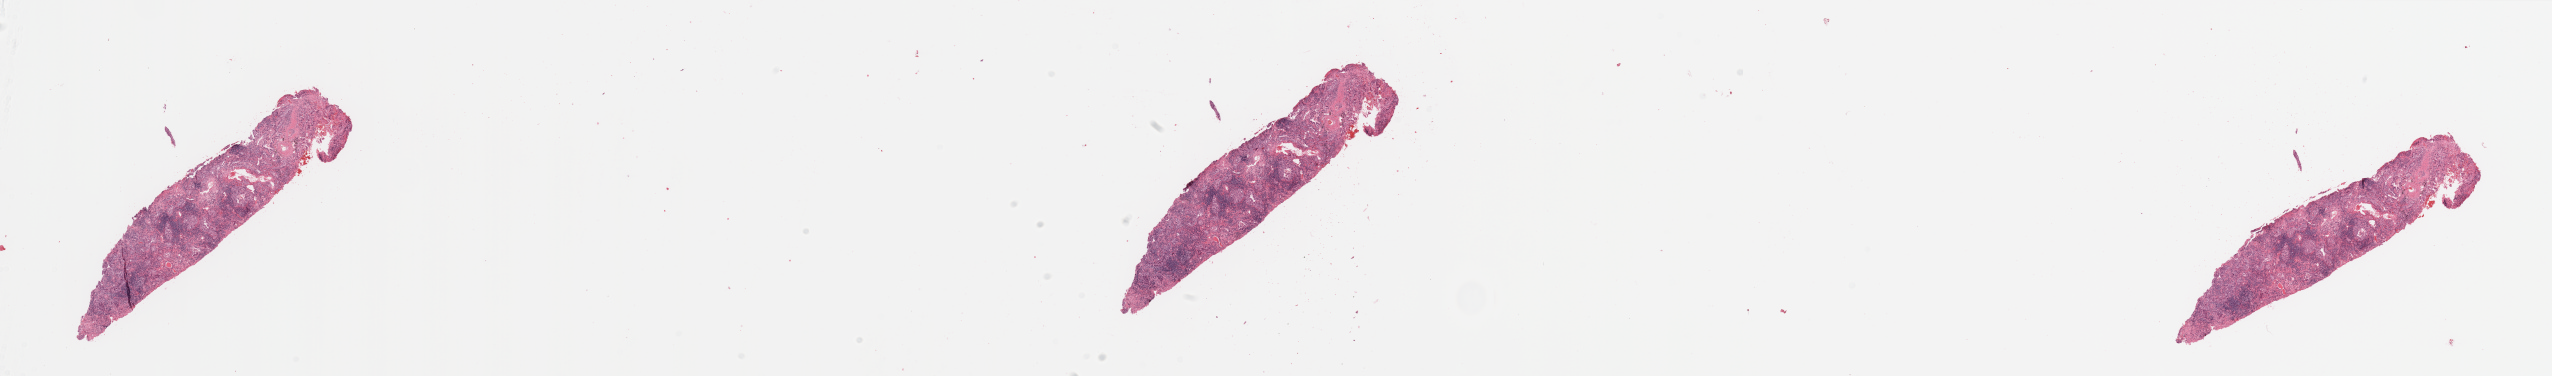
Digitized H&E-stained tissue section (whole slide), whole scanned area (about 40.4 x 5.9 mm) shown as a low-resolution overview. Tumour tissue sample, sampled site: lung. 81-year-old male patient. Histologic grade: G2 (moderately differentiated). Slide review estimates, as recorded: tumour nuclei 65%, necrosis 5%.
AJCC pathologic stage: IIA. Diagnosis: Adenocarcinoma, NOS. Primary tumour site (as recorded): right lower lobe.